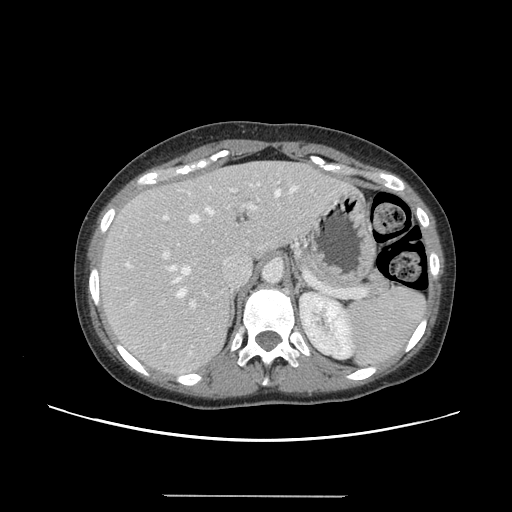
Contrast-enhanced abdominal CT, one axial slice. Slice 99 of 144 in the series (ordered by position). 120 kVp. Intravenous contrast given. Soft-tissue window (W 400 / L 40 HU). 2.5 mm slice thickness. 512 × 512 image matrix, field of view 380 × 380 mm. Female patient, age 53 years. From the clinical record (not read from this slice): diagnosis: colorectal cancer liver metastases, imaged before liver resection; multiple liver metastases: yes; largest metastasis: 1.1 cm; disease in both lobes: no.
Structures marked on this image (manually delineated by an expert):
- hepatic veins: bounding box (x1, y1, x2, y2) in pixels: (128, 187, 296, 297)
- liver: (99, 162, 347, 376)
- planned liver remnant (the part of the liver to remain after resection): (100, 163, 305, 300)
- portal vein (with intrahepatic branches): (162, 181, 280, 309)